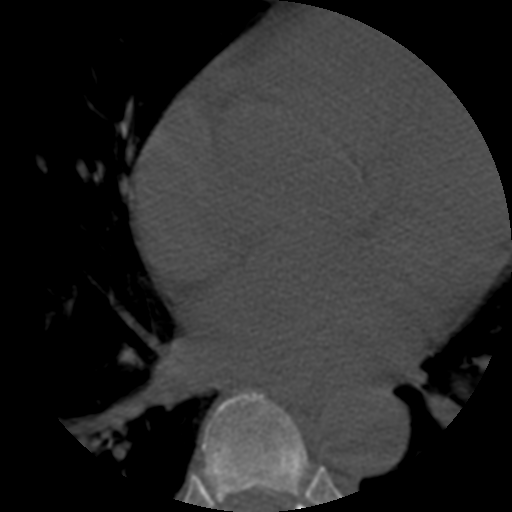
CT including the spine, one axial slice. Position 345 of 508 along the scan axis. Reconstruction kernel STANDARD. Bone window (W 1800 / L 400 HU). 512 × 512 image matrix, field of view 160 × 160 mm. Patient age 57 years. Case-level facts recorded for this patient, not image findings: primary cancer: prostate.
Outlined on this slice (semi-automatically segmented with operator editing):
- T6 vertebra: bounding box <202,391,311,504> (left, top, right, bottom; pixels)
- T7 vertebra: <295,488,304,509>